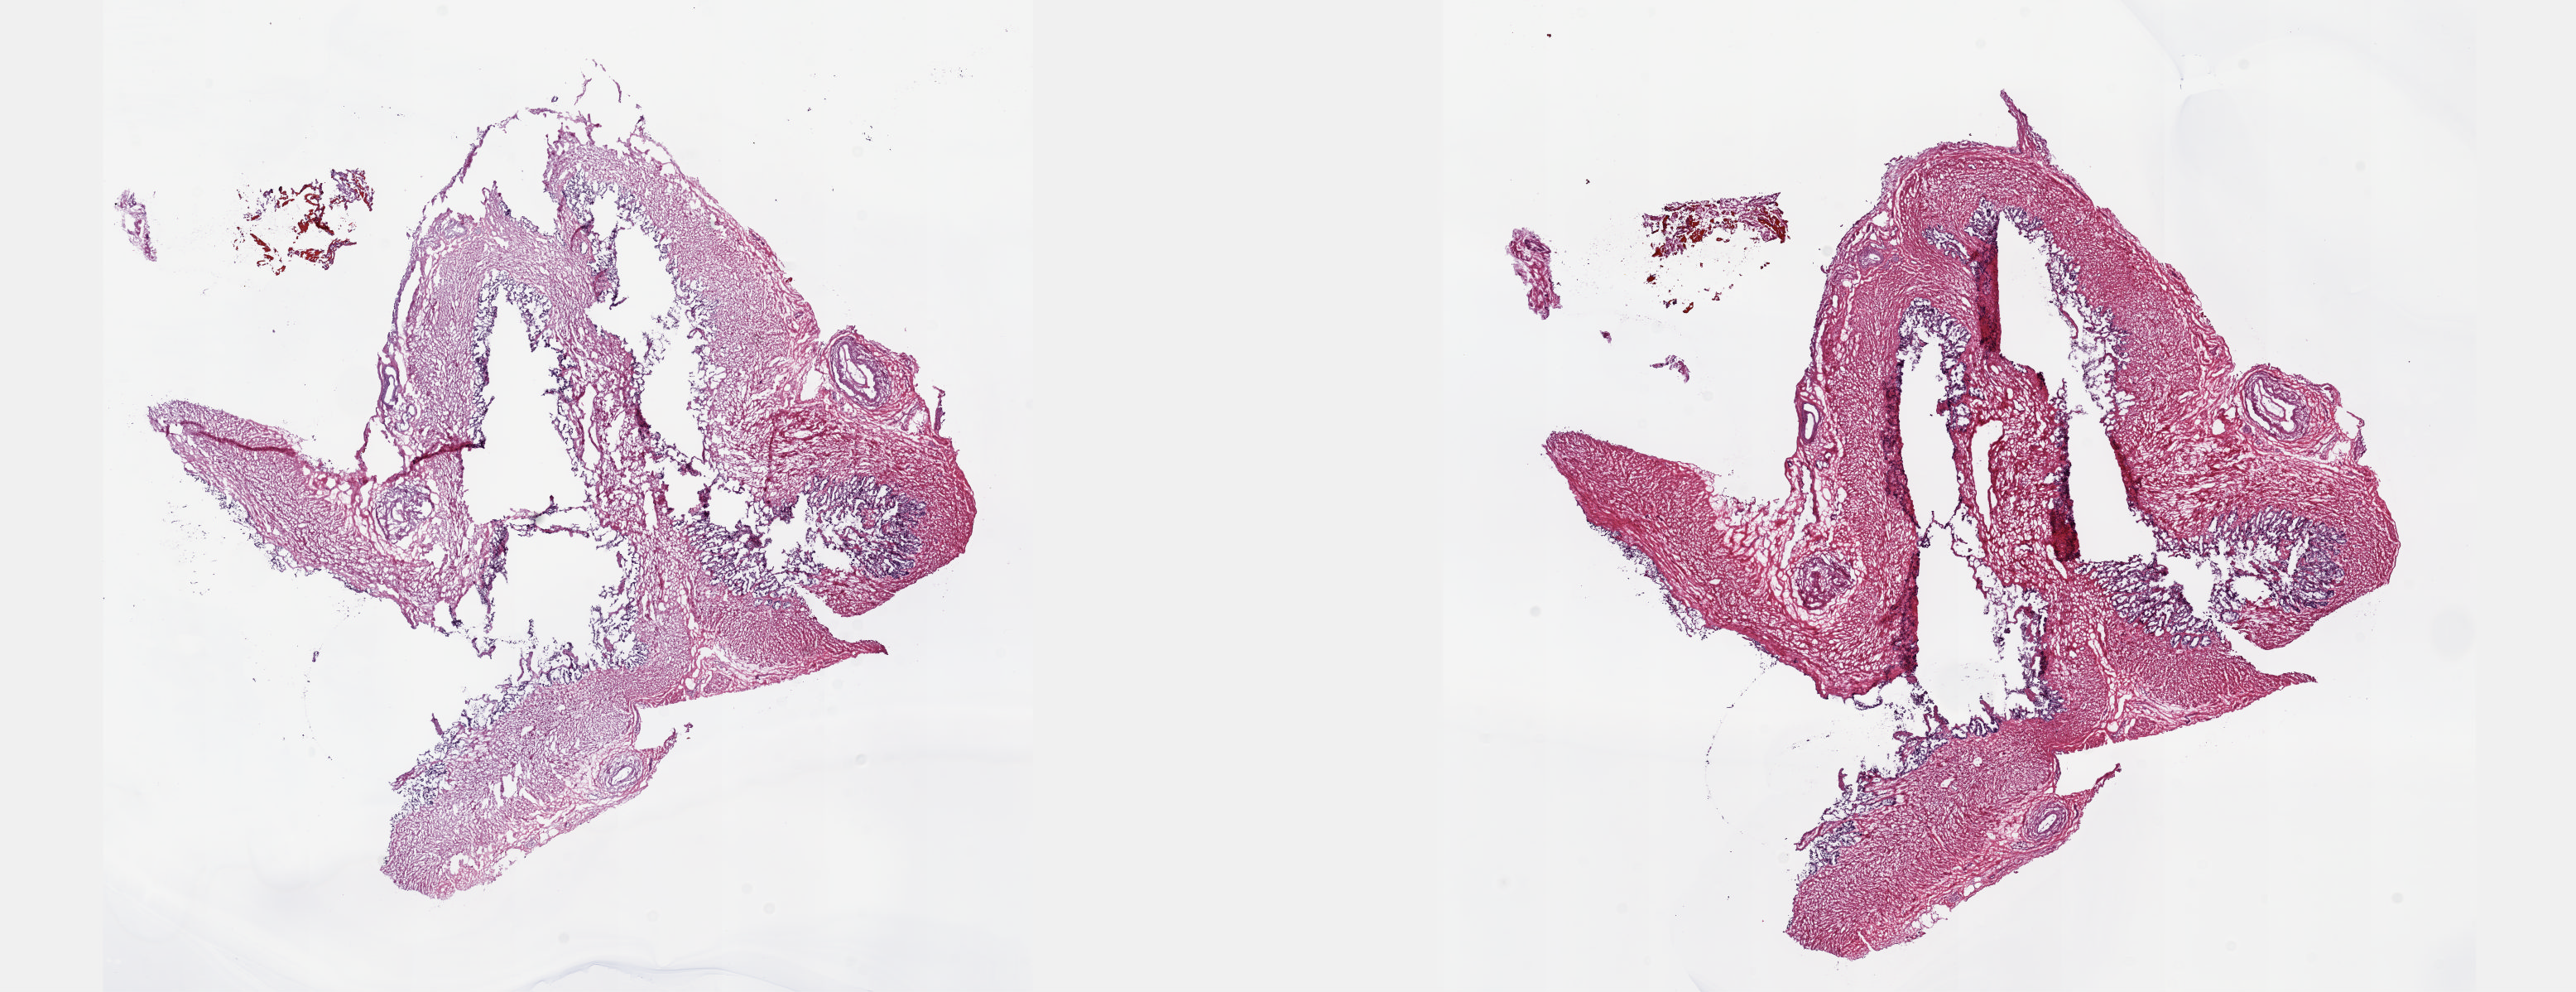
Digitized H&E tissue section (whole slide), a low-resolution overview of the entire scanned area, about 25.1 x 9.7 mm (from a 20x scan); frozen section from the top of the tissue portion; solid tissue normal (non-tumour tissue) sample from the prostate. Patient: male, age at initial diagnosis 65 years. Slide review estimates, as recorded: tumour cells 0%, tumour nuclei 0%, normal cells 18%, stromal cells 82%, necrosis 0%. Inflammatory infiltration, as recorded: lymphocyte infiltration 2%, monocyte infiltration 0%, neutrophil infiltration 0%.
This section: solid tissue normal (non-tumour) sample from the same patient. Patient diagnosis: Adenocarcinoma, NOS (prostate gland).